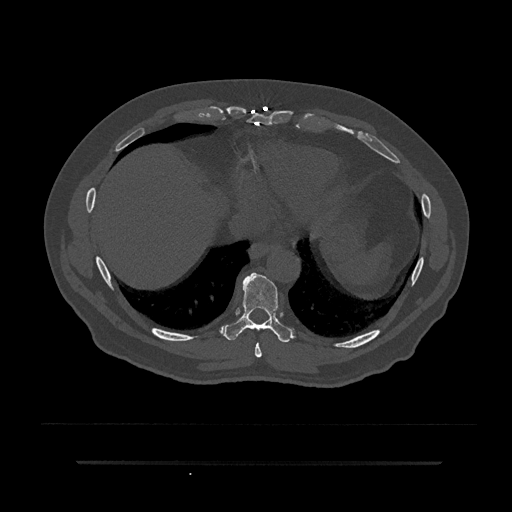
CT including the spine, one axial slice. Reconstruction kernel Br40s/3. Bone window (W 1800 / L 400 HU). 0.5 mm slice thickness. 512 × 512 image matrix, field of view 464 × 464 mm. Patient: male, 59 years. From the clinical record (not read from this slice): primary cancer: bile ducts; vertebrae with lytic lesions (as recorded): T10.
Outlined on this slice (semi-automatically segmented with operator editing):
- T8 vertebra: bounding box <255,343,262,358> (left, top, right, bottom; pixels)
- T9 vertebra: <223,272,293,343>